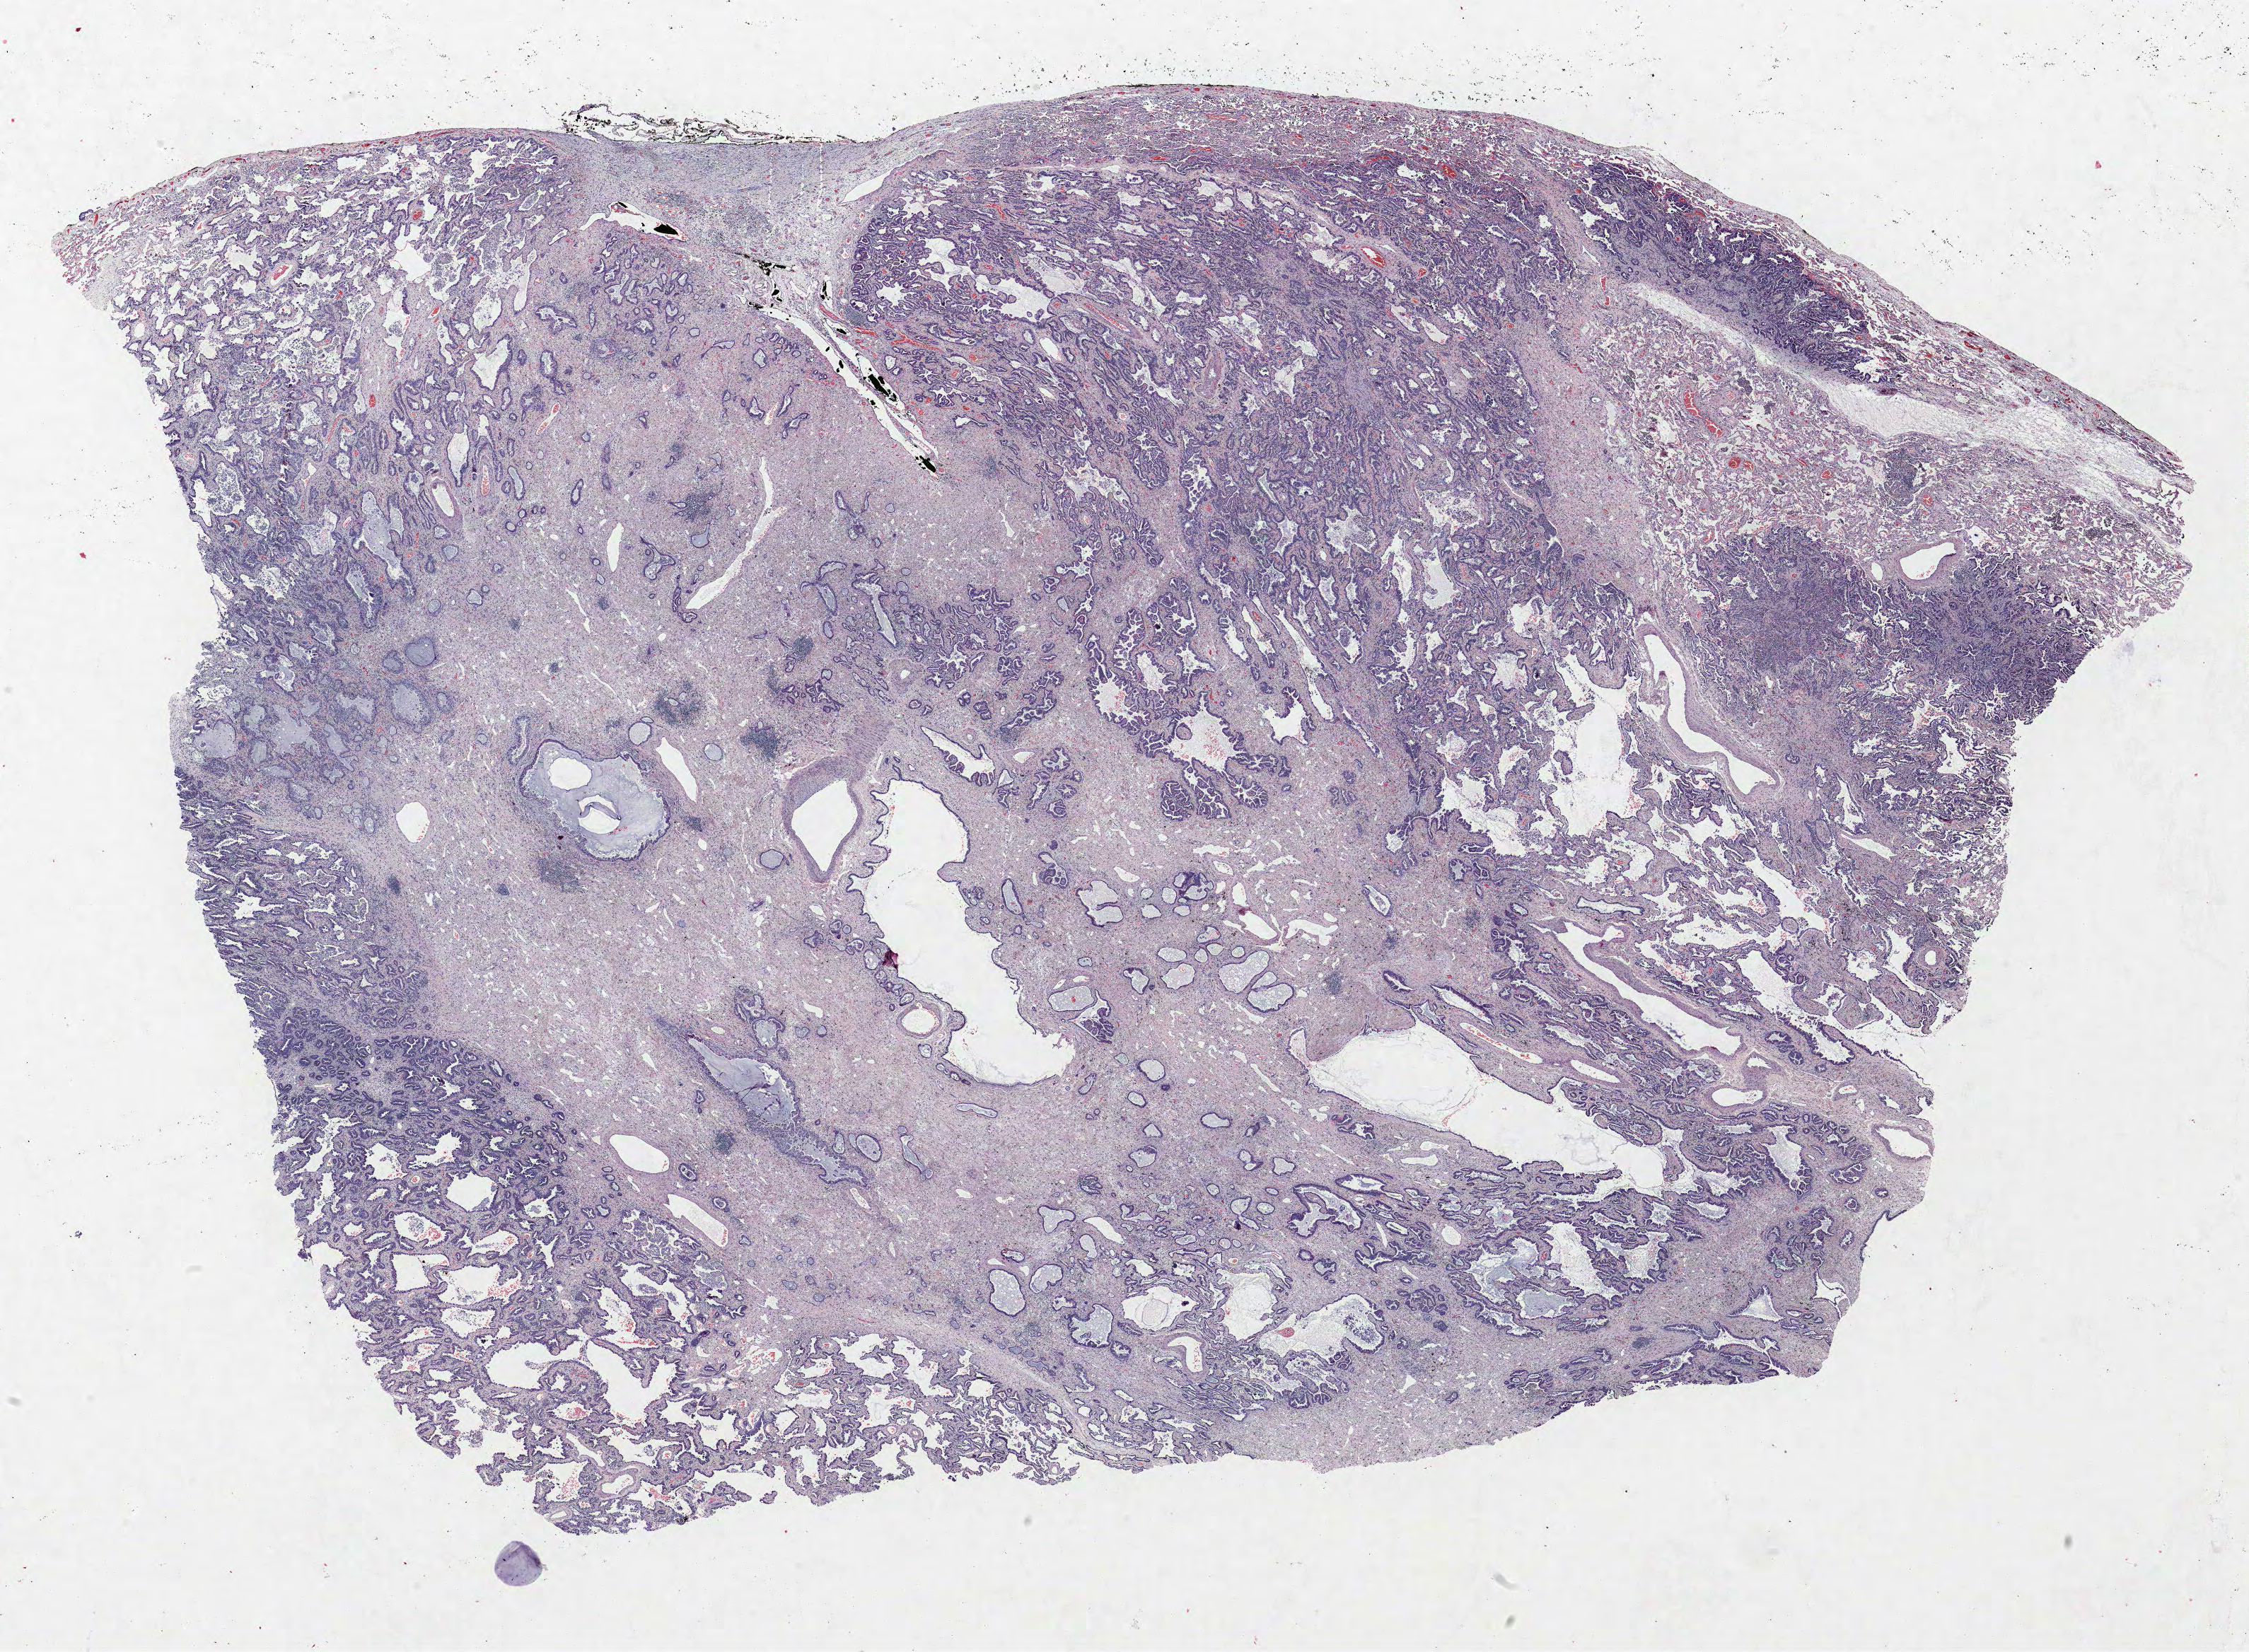
H&E-stained whole-slide image — shown as a low-resolution overview of the whole scanned area (about 25.4 x 18.7 mm); formalin-fixed paraffin-embedded (FFPE) section; lung. Male patient, aged 64 at enrolment. Former smoker at enrolment. Grade: well differentiated (G1).
• stage (AJCC 6th edition): IB
• primary tumour location (clinical record): right upper lobe
• tumour size (pathology): 45 mm
• participant's lung-cancer diagnosis: Adenocarcinoma, NOS